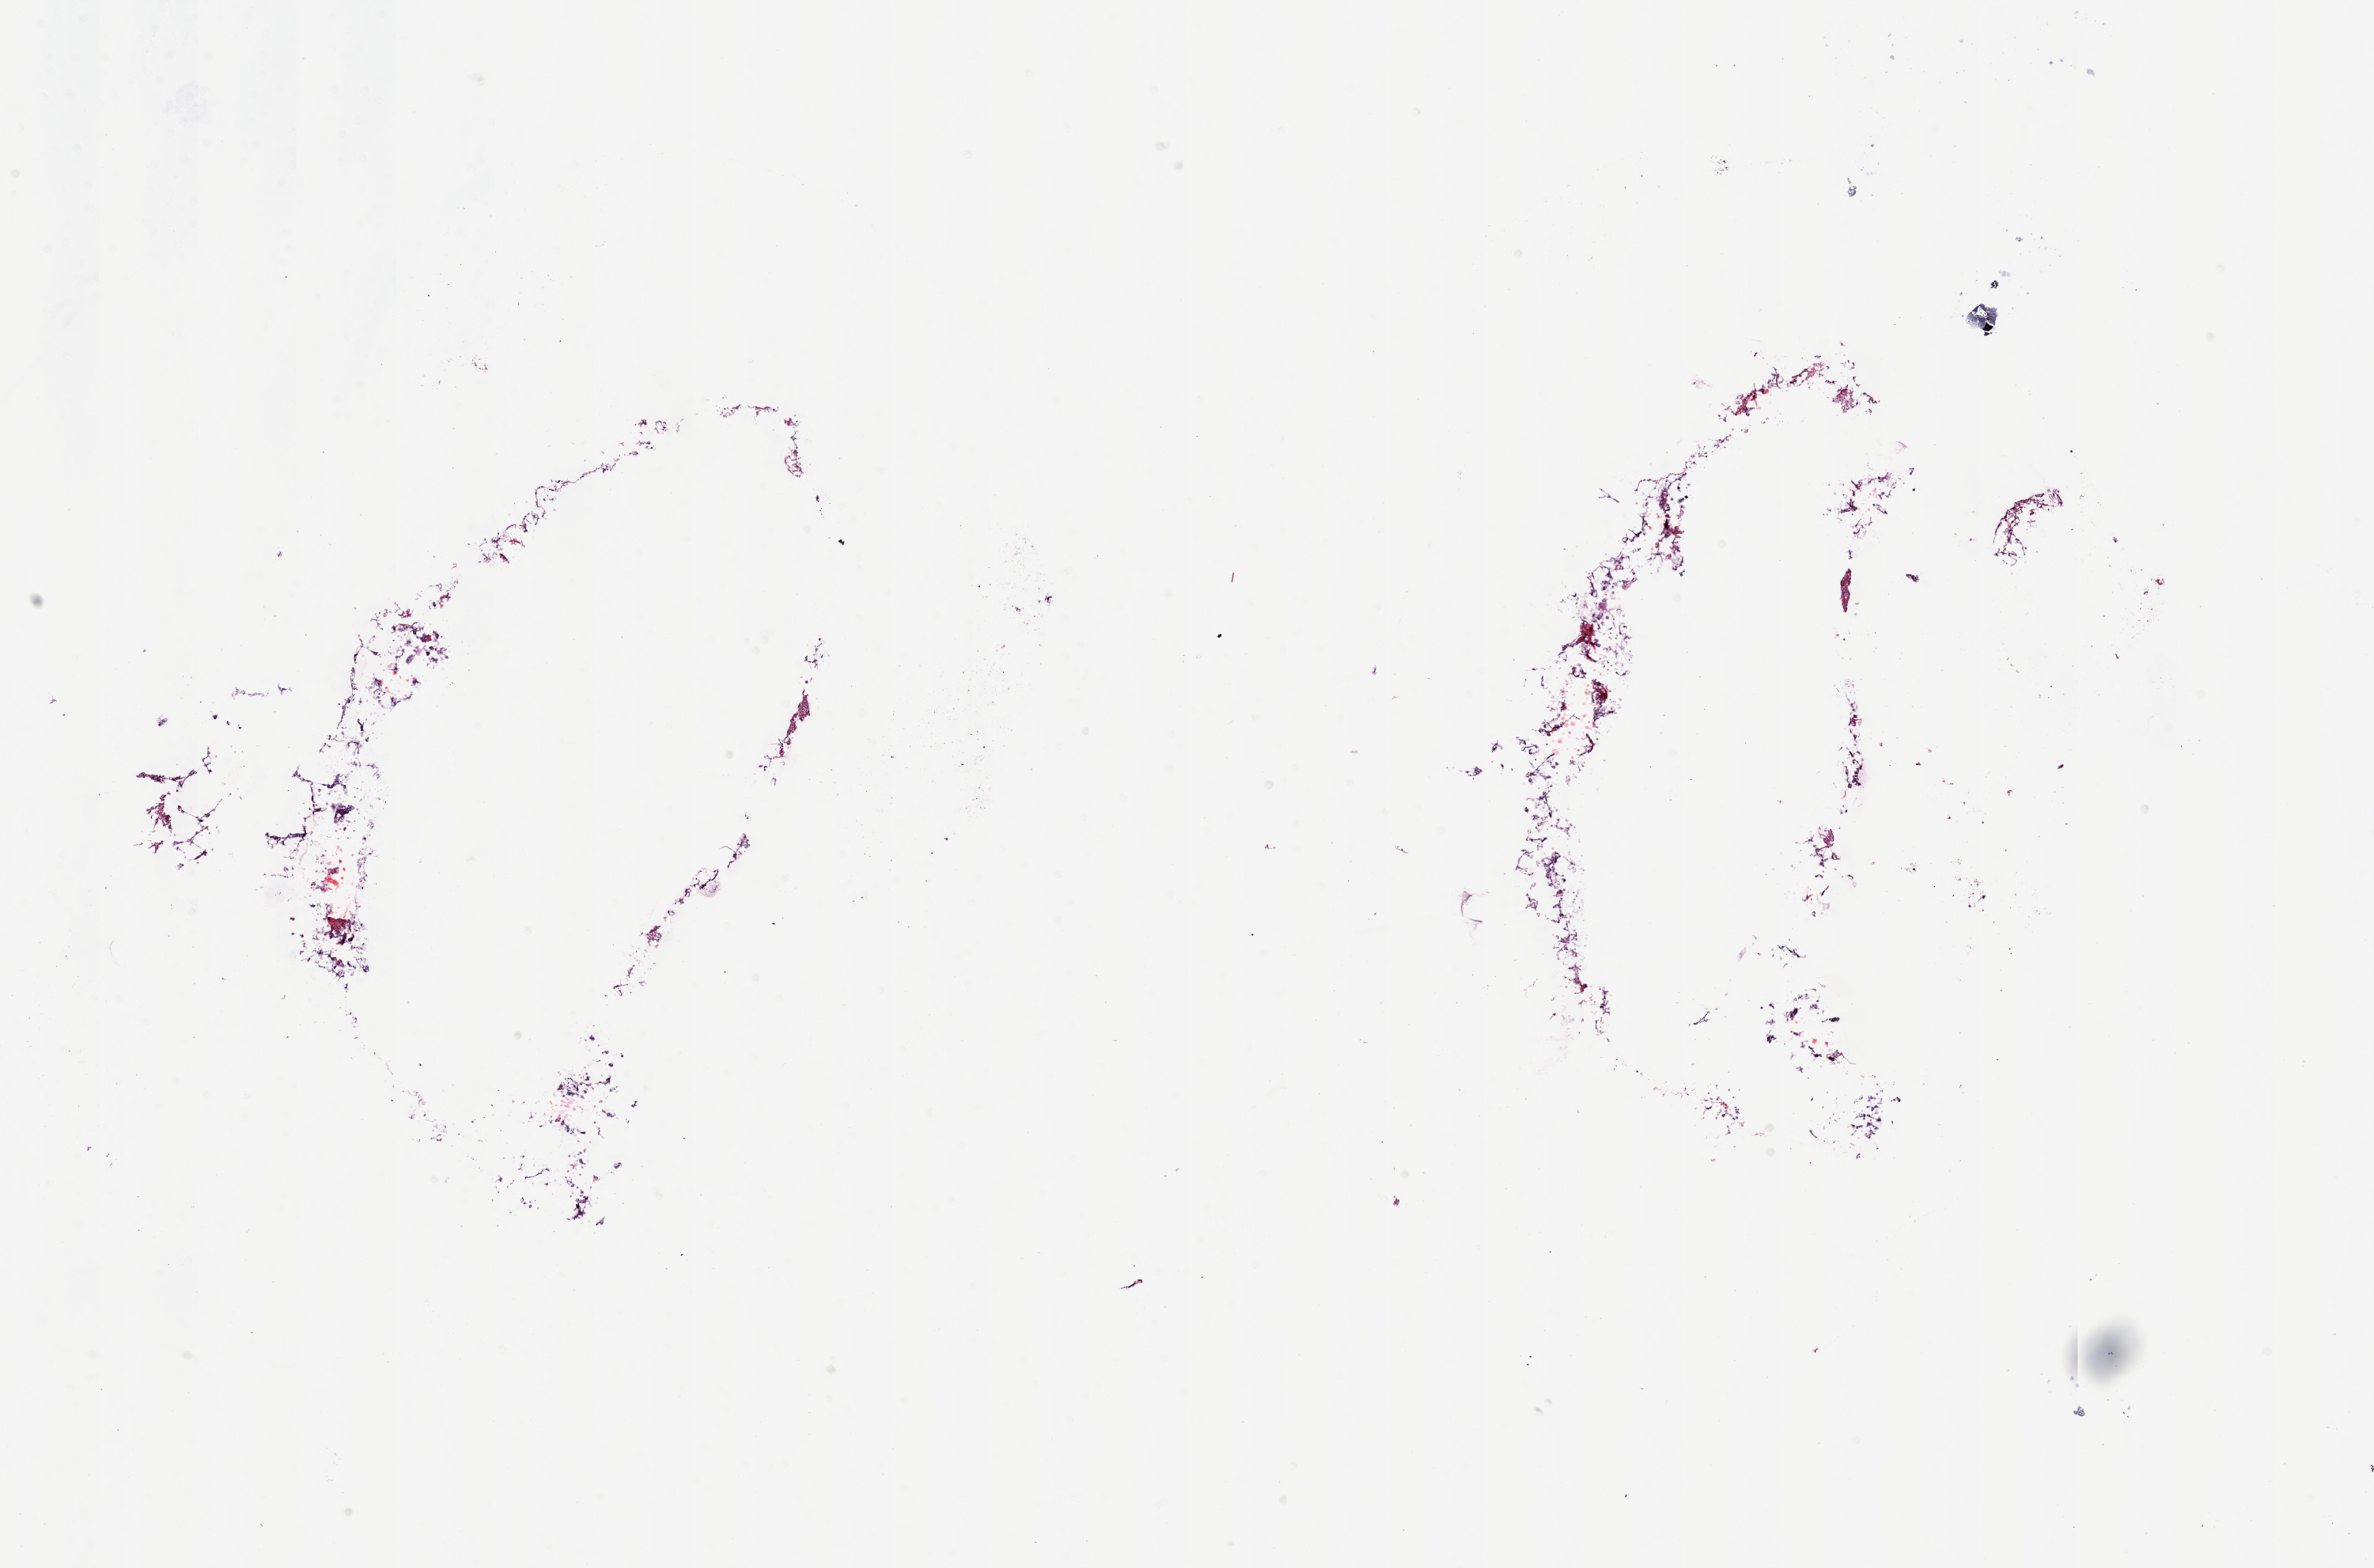
H&E whole-slide image, shown as a low-resolution overview of the whole scanned area (about 23.8 x 15.7 mm). Frozen section. Solid tissue normal (non-tumour tissue) sample from the breast. Female patient; age at initial diagnosis 56 years. Composition of this section per pathologist review: tumour cells 0%, normal cells 100%. Inflammatory infiltration, as recorded: lymphocyte infiltration 0%, monocyte infiltration 0%, neutrophil infiltration 0%.
This section: solid tissue normal (non-tumour) sample from the same patient. Patient diagnosis: Infiltrating duct carcinoma, NOS.